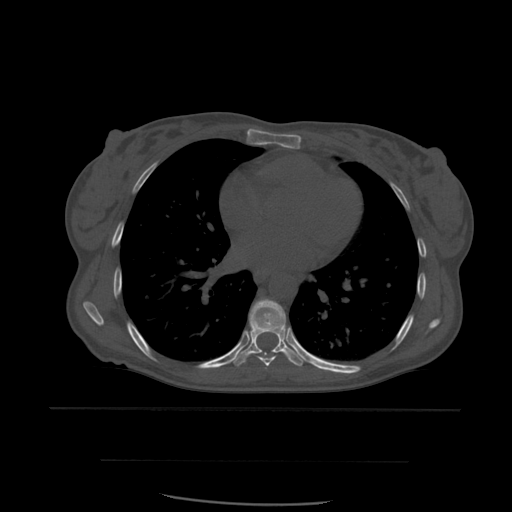
CT including the spine, one axial slice. Position 364 of 574 along the scan axis. Bone window (W 1800 / L 400 HU). 512 × 512 image matrix. Patient age 48 years. Case-level facts recorded for this patient, not image findings: primary cancer: lung.
Annotated regions visible in this slice (semi-automatic segmentation, software-assisted and operator-edited):
- T6 vertebra: bounding box (x1, y1, x2, y2) in pixels: (250, 322, 285, 337)
- T7 vertebra: (258, 353, 277, 369)
- T8 vertebra: (232, 299, 304, 367)